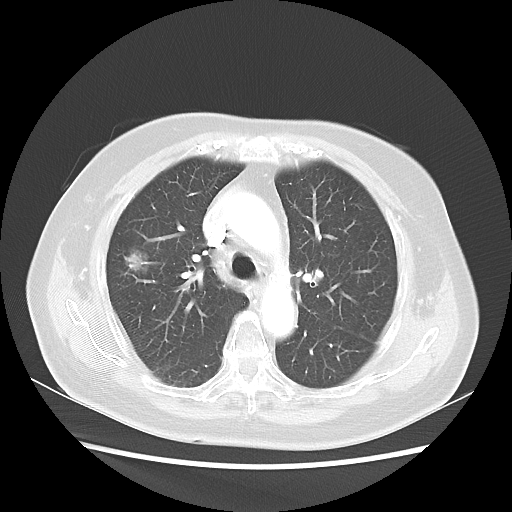
Chest CT, one axial slice; 100 kVp; lung window (W 1500 / L -600 HU); 5 mm slice thickness; 512 × 512 image matrix, field of view 360 × 360 mm. Female patient, age 75 years. Case-level facts recorded for this patient, not image findings: clinical TNM (as recorded): T1c N0 M0.
Outlined on this slice (bounding box drawn by a radiologist):
- lung tumour (recorded histology: adenocarcinoma): bounding box (x1, y1, x2, y2) in pixels: (116, 242, 154, 281)